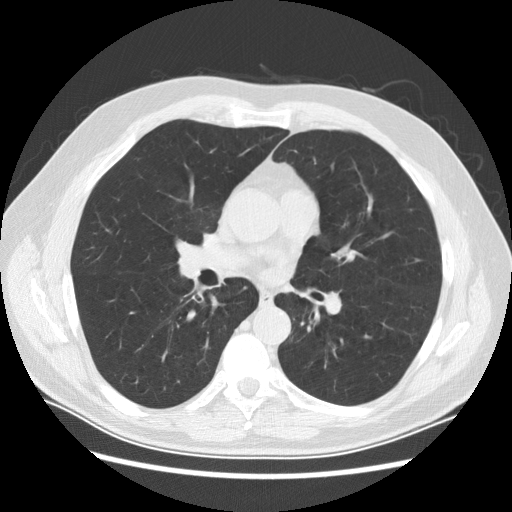
Low-dose screening chest CT, axial slice; baseline screening round; lung window (W 1500 / L -600 HU); slice 116 of 241 in the series; 512 × 512 image matrix. Male, age 61 years at enrolment. Former smoker at enrolment.
• Lesion marked by an expert reader, bounding box <225,277,253,311> (left, top, right, bottom; pixels).
• Screening reader's record for this exam: no non-calcified nodule ≥4 mm recorded.
• Later outcome: lung cancer diagnosed 756 days after this screen — squamous cell carcinoma, keratinizing, NOS, right lower lobe, stage IIIB (AJCC 6th edition), 40 mm at pathology.